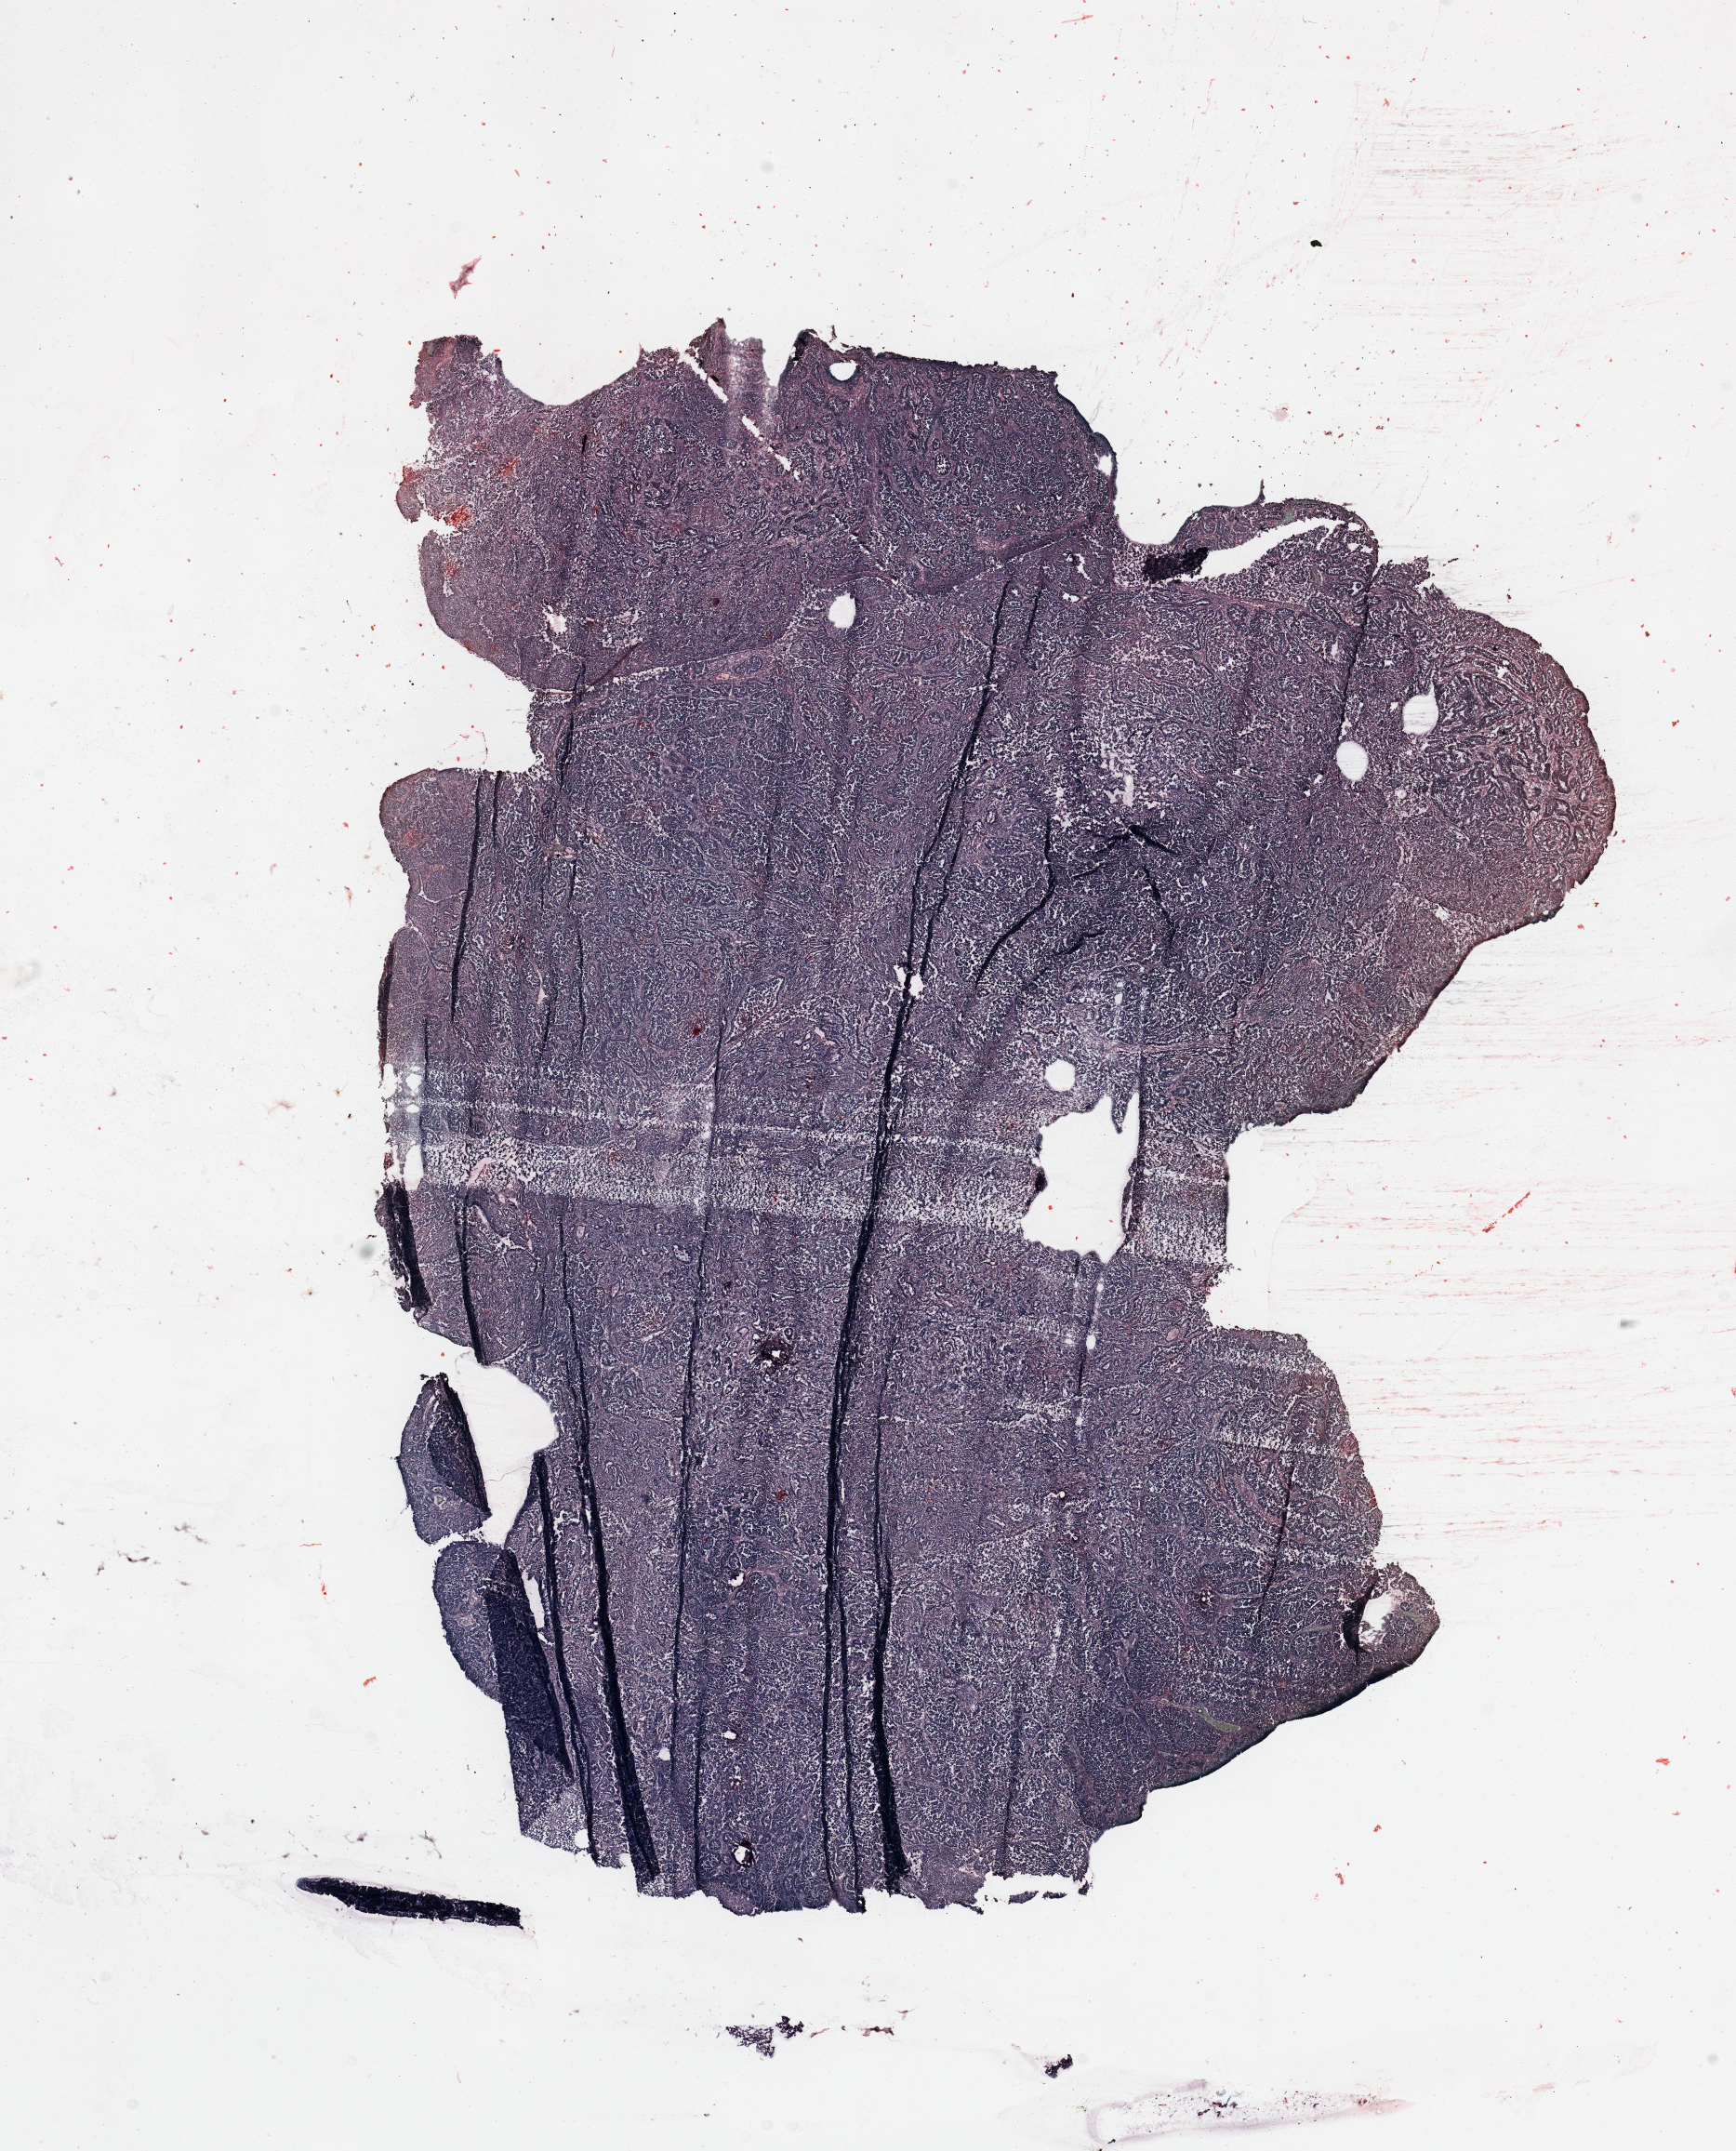
H&E-stained whole-slide image, whole scanned area (about 14.8 x 18.3 mm, acquisition: 20x scan) shown as a low-resolution overview; uterus, tumour tissue. Patient: female, age 60 years.
Diagnosis: Endometrioid adenocarcinoma, NOS.